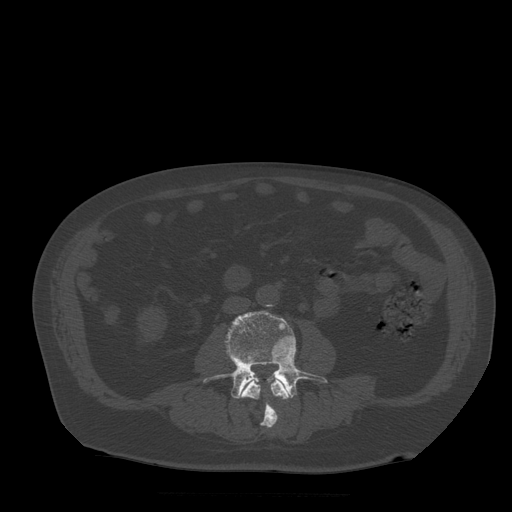
CT including the spine, one axial slice; position 124 of 522 along the scan axis; bone window (W 1800 / L 400 HU); 1.25 mm slice thickness; 512 × 512 image matrix, field of view 420 × 420 mm. Patient age 72 years. Case-level facts recorded for this patient, not image findings: primary cancer: prostate.
Outlined on this slice (semi-automatic segmentation, software-assisted and operator-edited):
- L3 vertebra: bounding box <240,379,291,428> (left, top, right, bottom; pixels)
- L4 vertebra: <204,311,328,399>